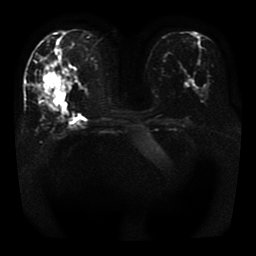
Breast MRI, one axial slice; slice 17 of 41 in the series (ordered by position); diffusion-weighted series; image 2 of 4 stored at this slice position (different b-values; order by instance number); 1.5 T; 256 × 256 image matrix, field of view 330 × 330 mm. Female patient.
Annotated regions visible in this slice (outlined manually by an expert reader):
- tumour on diffusion-weighted imaging: bounding box (x1, y1, x2, y2) in pixels: (44, 72, 61, 96)